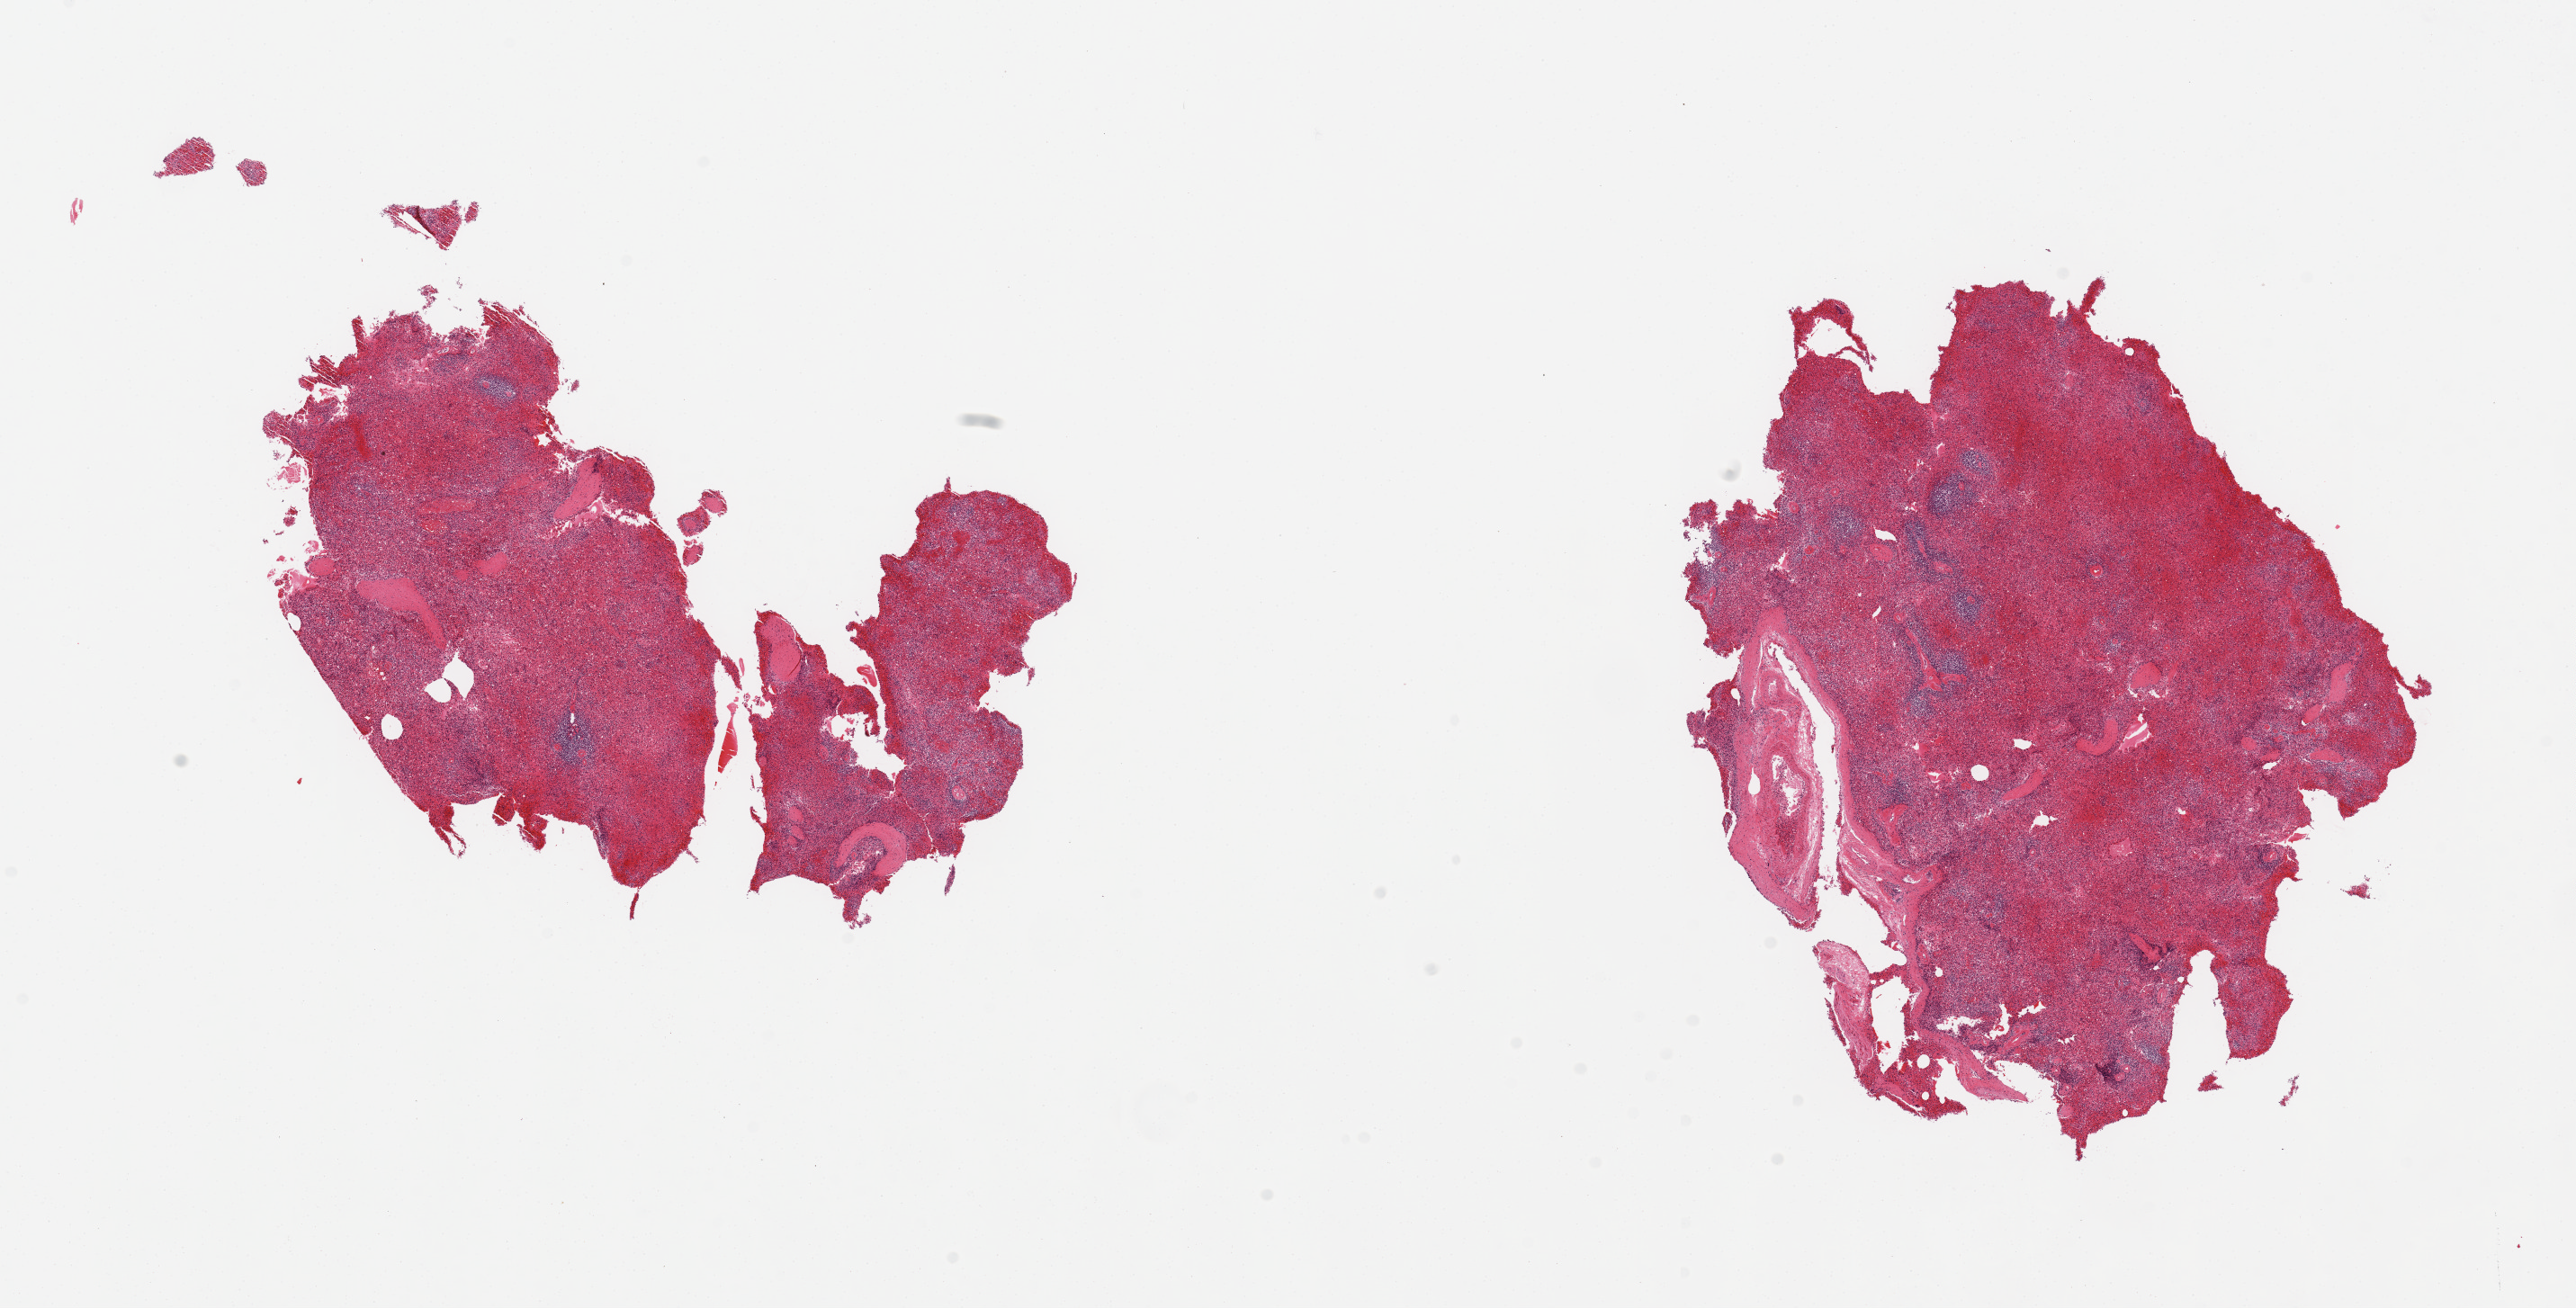
Whole-slide image, H&E stain, low-resolution overview of the scanned area, about 22.6 x 11.5 mm, PAXgene-fixed, paraffin-embedded tissue, section of spleen (target tissue), donor tissue sample. Donor: male.
Pathologist's review note for this sample: 2 pieces; congestion.